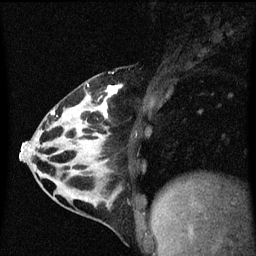
Breast MRI (dynamic contrast-enhanced), one sagittal slice; slice 26 of 60 in the series (ordered by position); dynamic contrast-enhanced series, image 2 of 3 at this slice position (ordered by acquisition); 1.5 T; TE 4.2 ms, TR 8.4 ms; 2 mm slice thickness; 256 × 256 image matrix, field of view 200 × 200 mm. Patient: female, 32 years.
Structures marked on this image (semi-automatically segmented with operator editing):
- analysis volume of interest (the breast-tissue region the enhancement analysis was run in; not a lesion): box from (x=34, y=74) to (x=149, y=169) px
- tumour enhancement mask (voxels above the 70 % enhancement threshold inside the analysis volume of interest): (x=52, y=84)–(x=123, y=117)